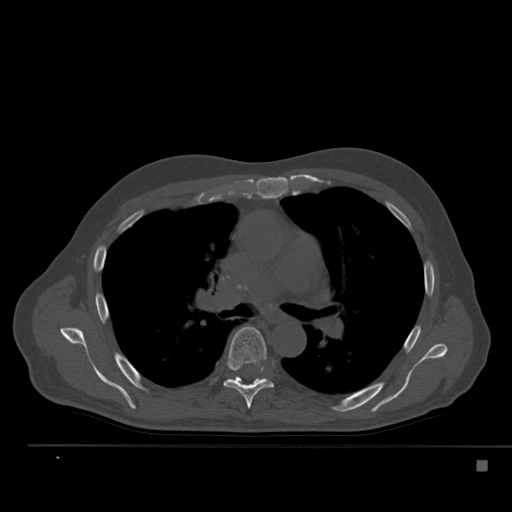
CT including the spine, one axial slice. Slice 346 of 517 in the series (ordered by position). Bone window (W 1800 / L 400 HU). 512 × 512 image matrix. Patient: male, 70 years. From the clinical record (not read from this slice): primary cancer: renal; vertebrae with lytic lesions (as recorded): T4, T6, T10, T12, L3, L4, L5.
Outlined on this slice (semi-automatic segmentation, software-assisted and operator-edited):
- T6 vertebra: box from (x=223, y=327) to (x=273, y=409) px
- T7 vertebra: (x=230, y=377)–(x=266, y=381)